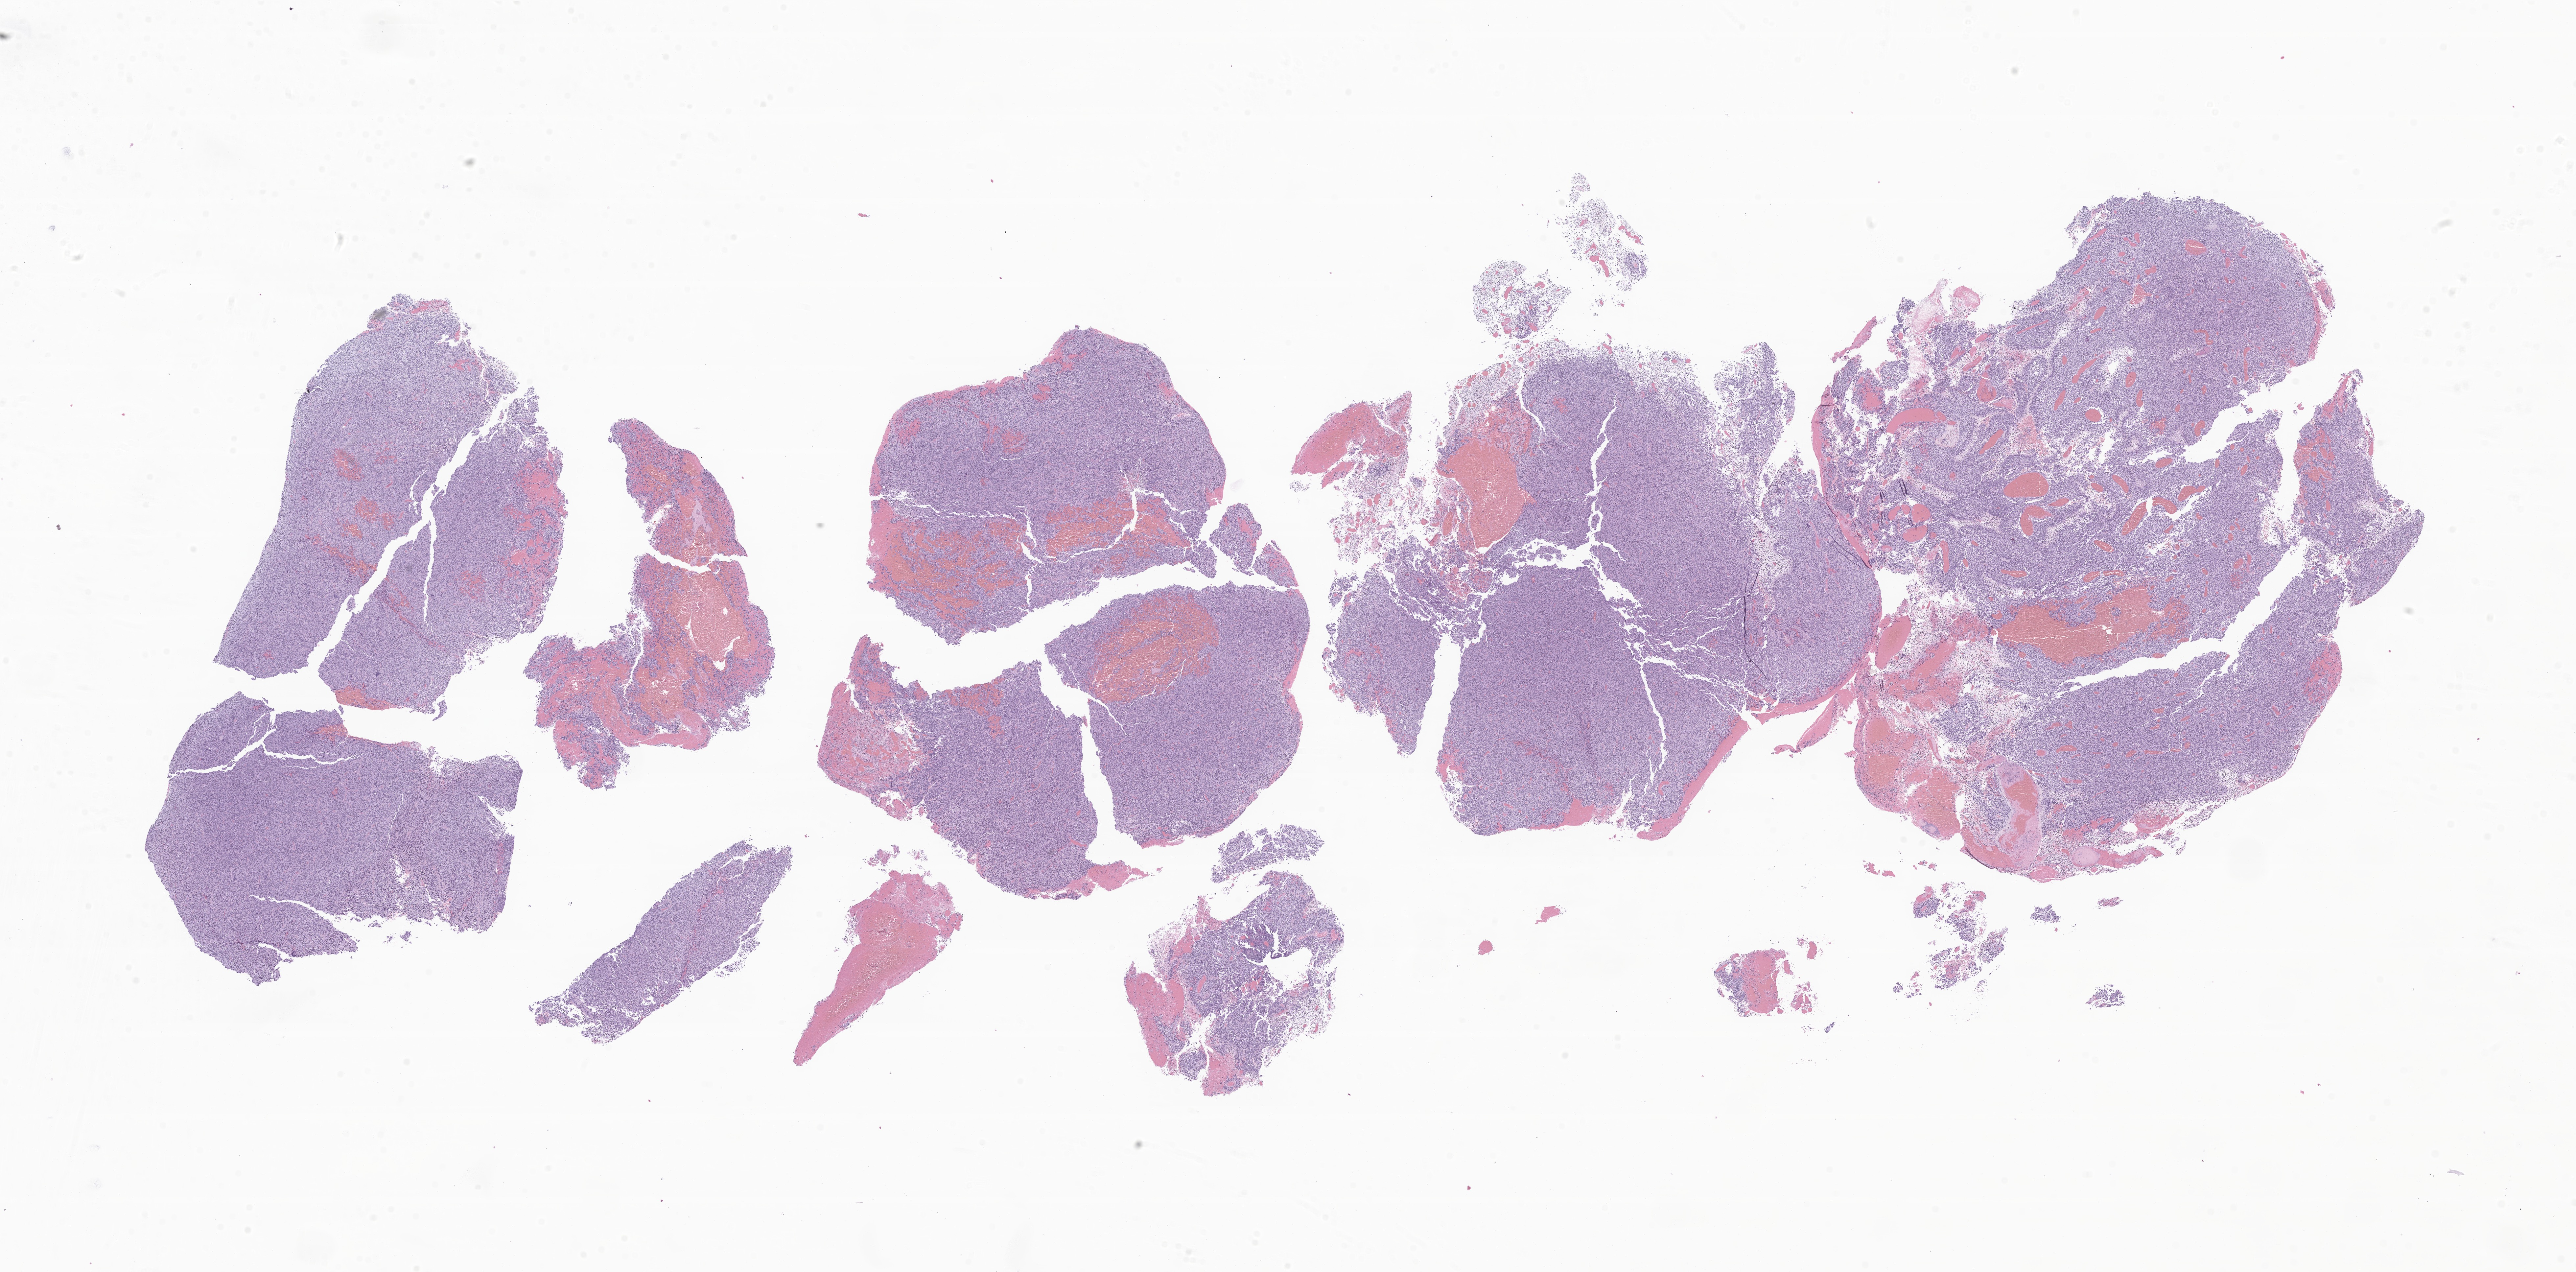
Whole-slide image, hematoxylin and eosin (H&E) stain of tumor tissue from the brain — a low-resolution overview of the entire scanned area, about 33.0 x 16.3 mm, formalin-fixed, paraffin-embedded (FFPE) tissue. Patient male; age 220 months (18 years 4 months).
Diagnosis (ICD-O-3 morphology term): Glioma, malignant.